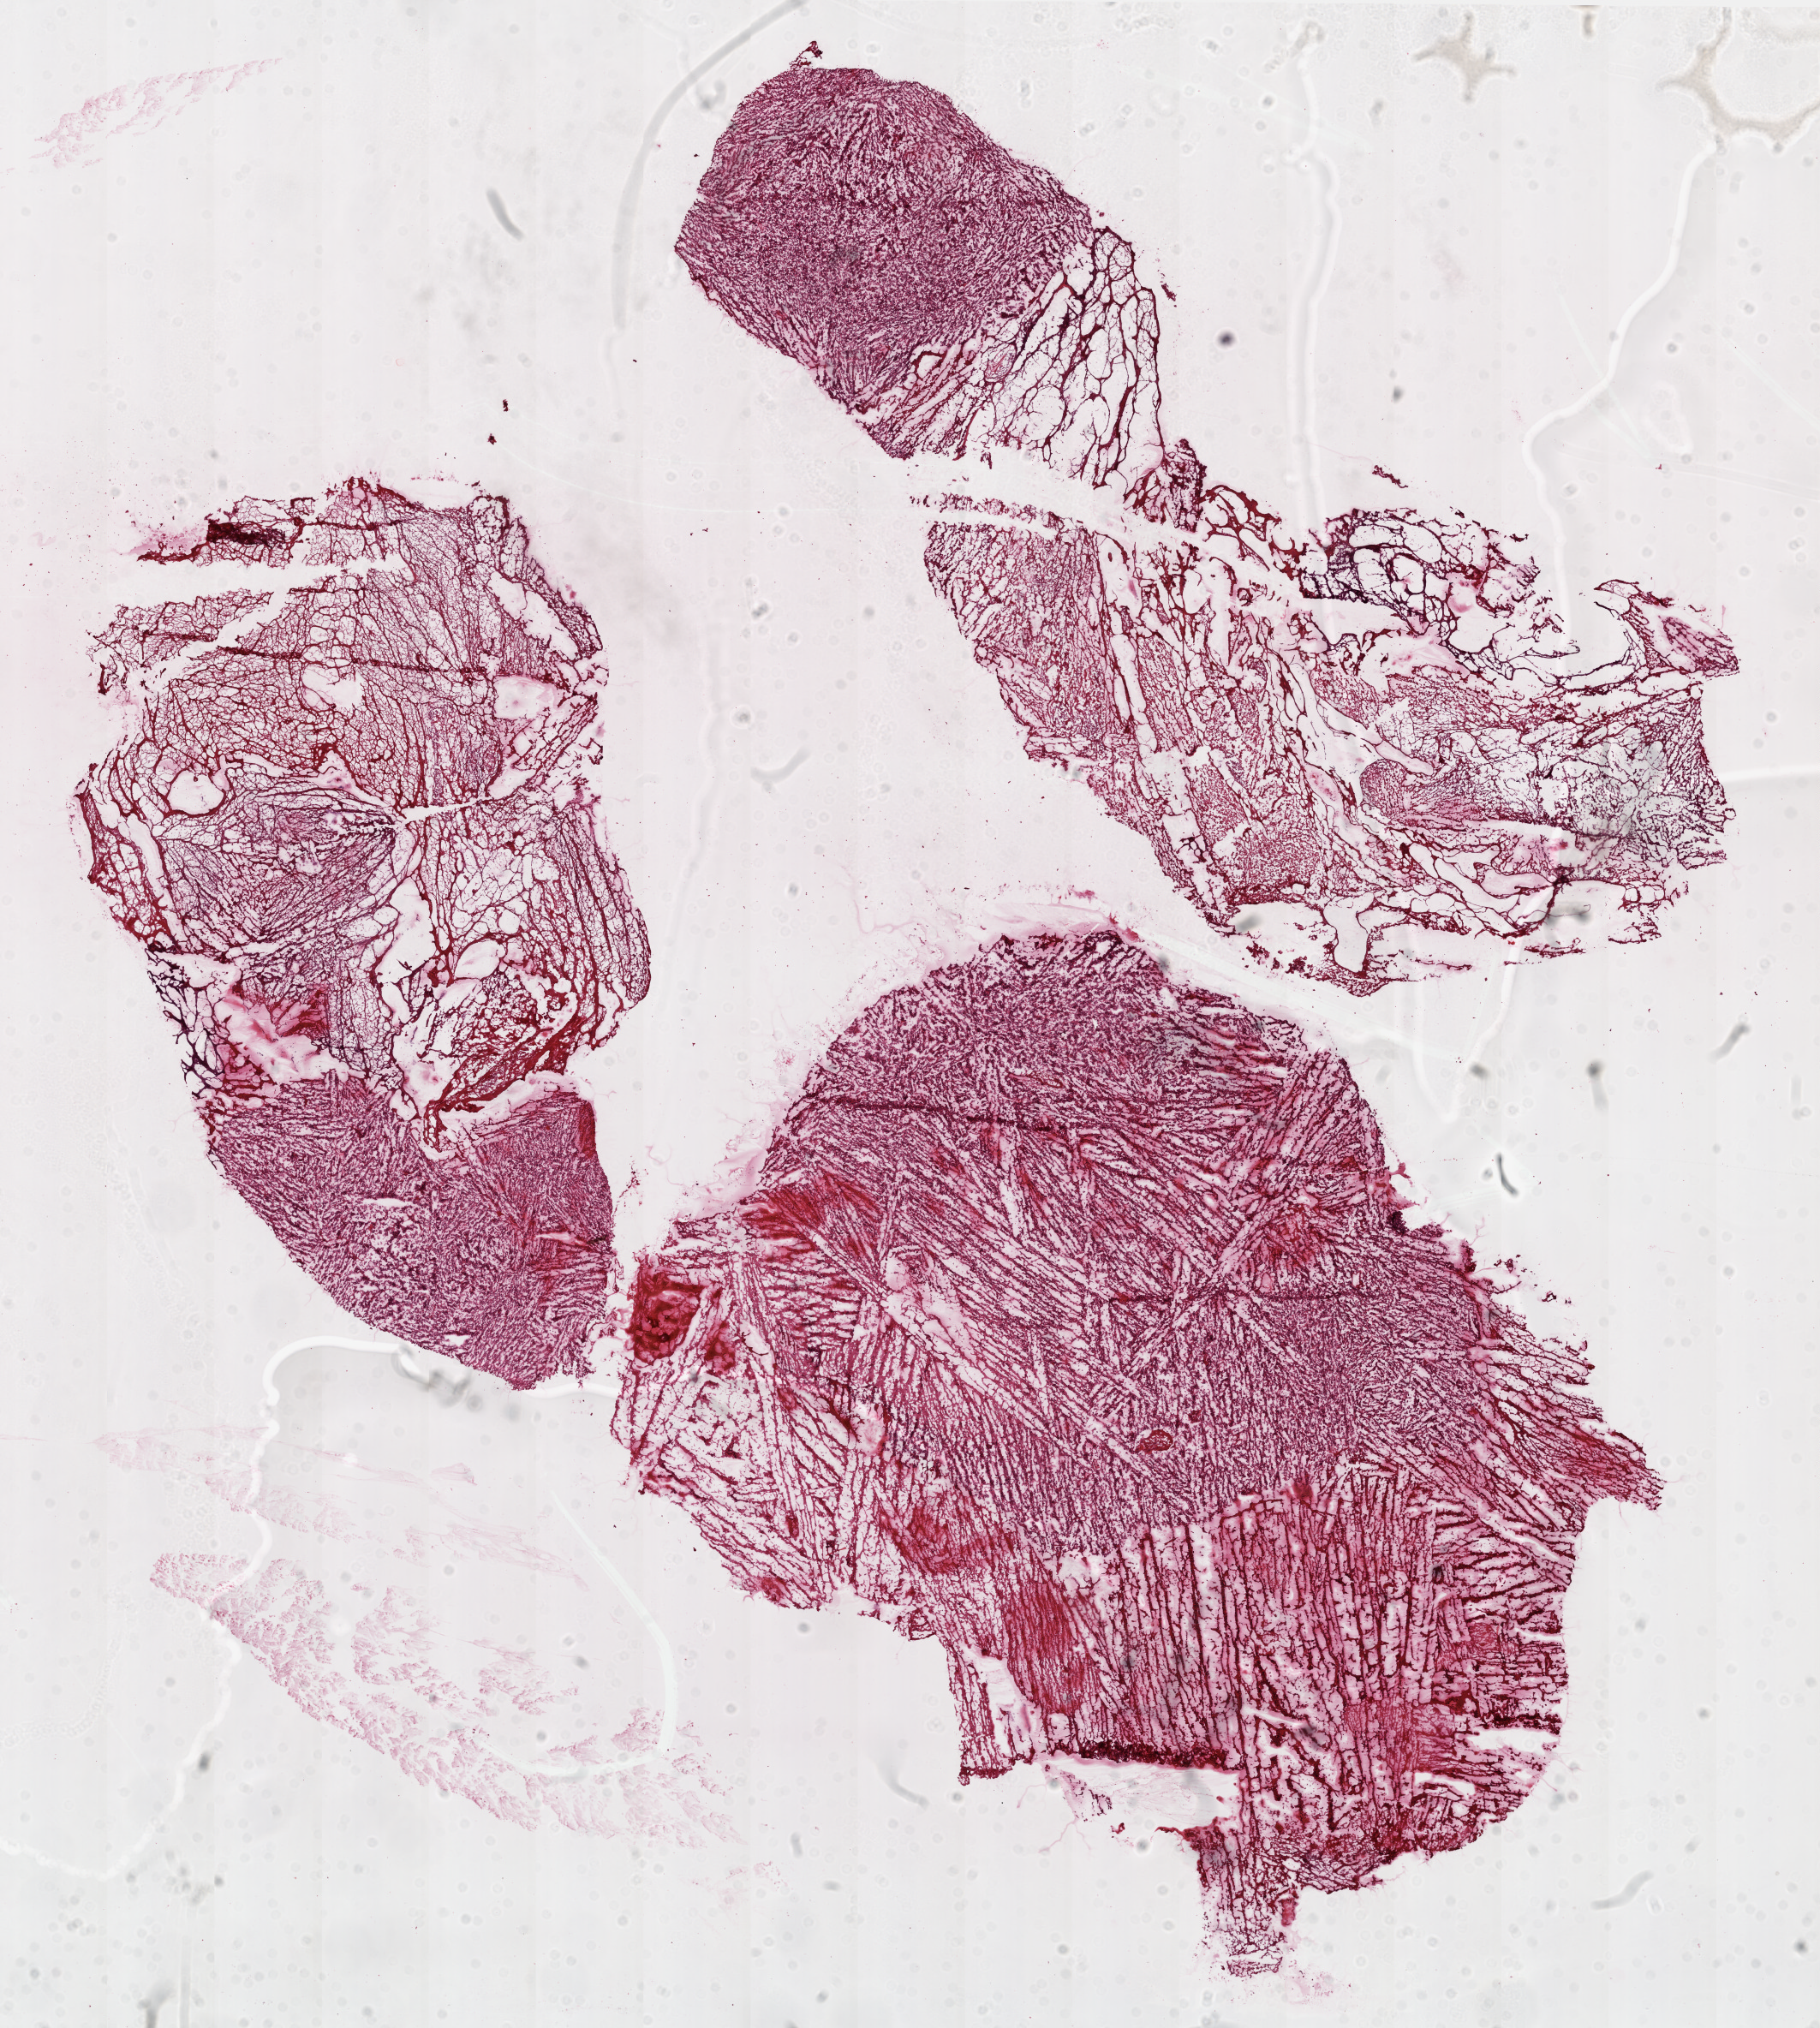
H&E whole-slide image — shown as a low-resolution overview of the whole scanned area (about 17.1 x 19.0 mm, acquisition: 20x scan), frozen section from the top of the tissue portion, primary tumour sample from the brain. Patient: female, age at initial diagnosis 85 years. Pathologist review of this section (percent, as recorded): tumour cells 50%, tumour nuclei 80%, normal cells 0%, stromal cells 0%, necrosis 50%.
• diagnosis: Glioblastoma